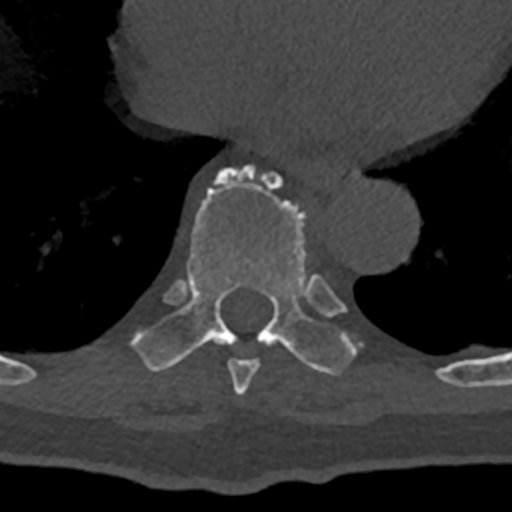
CT including the spine, one axial slice. Slice 670 of 797 in the series (ordered by position). Bone window (W 1800 / L 400 HU). 512 × 512 image matrix, field of view 160 × 160 mm. Patient: male, 74 years. Case-level facts recorded for this patient, not image findings: primary cancer: renal.
Structures marked on this image (semi-automatically segmented with operator editing):
- T8 vertebra: bounding box [x1, y1, x2, y2] px = [227, 358, 260, 395]
- T9 vertebra: [131, 166, 362, 376]